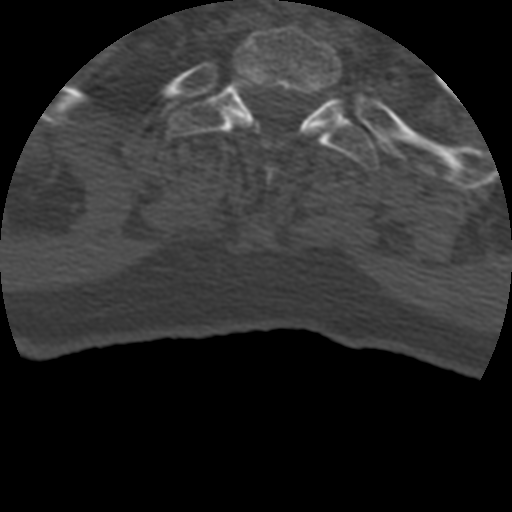
CT including the spine, one axial slice; slice 374 of 399 in the series (ordered by position); 120 kVp; bone window (W 1800 / L 400 HU); 512 × 512 image matrix, field of view 160 × 160 mm. Patient age 69 years. Case-level facts recorded for this patient, not image findings: primary cancer: prostate.
Structures marked on this image (semi-automatic segmentation, software-assisted and operator-edited):
- T1 vertebra: box from (x=234, y=27) to (x=352, y=144) px
- T2 vertebra: (x=167, y=77)–(x=379, y=171)